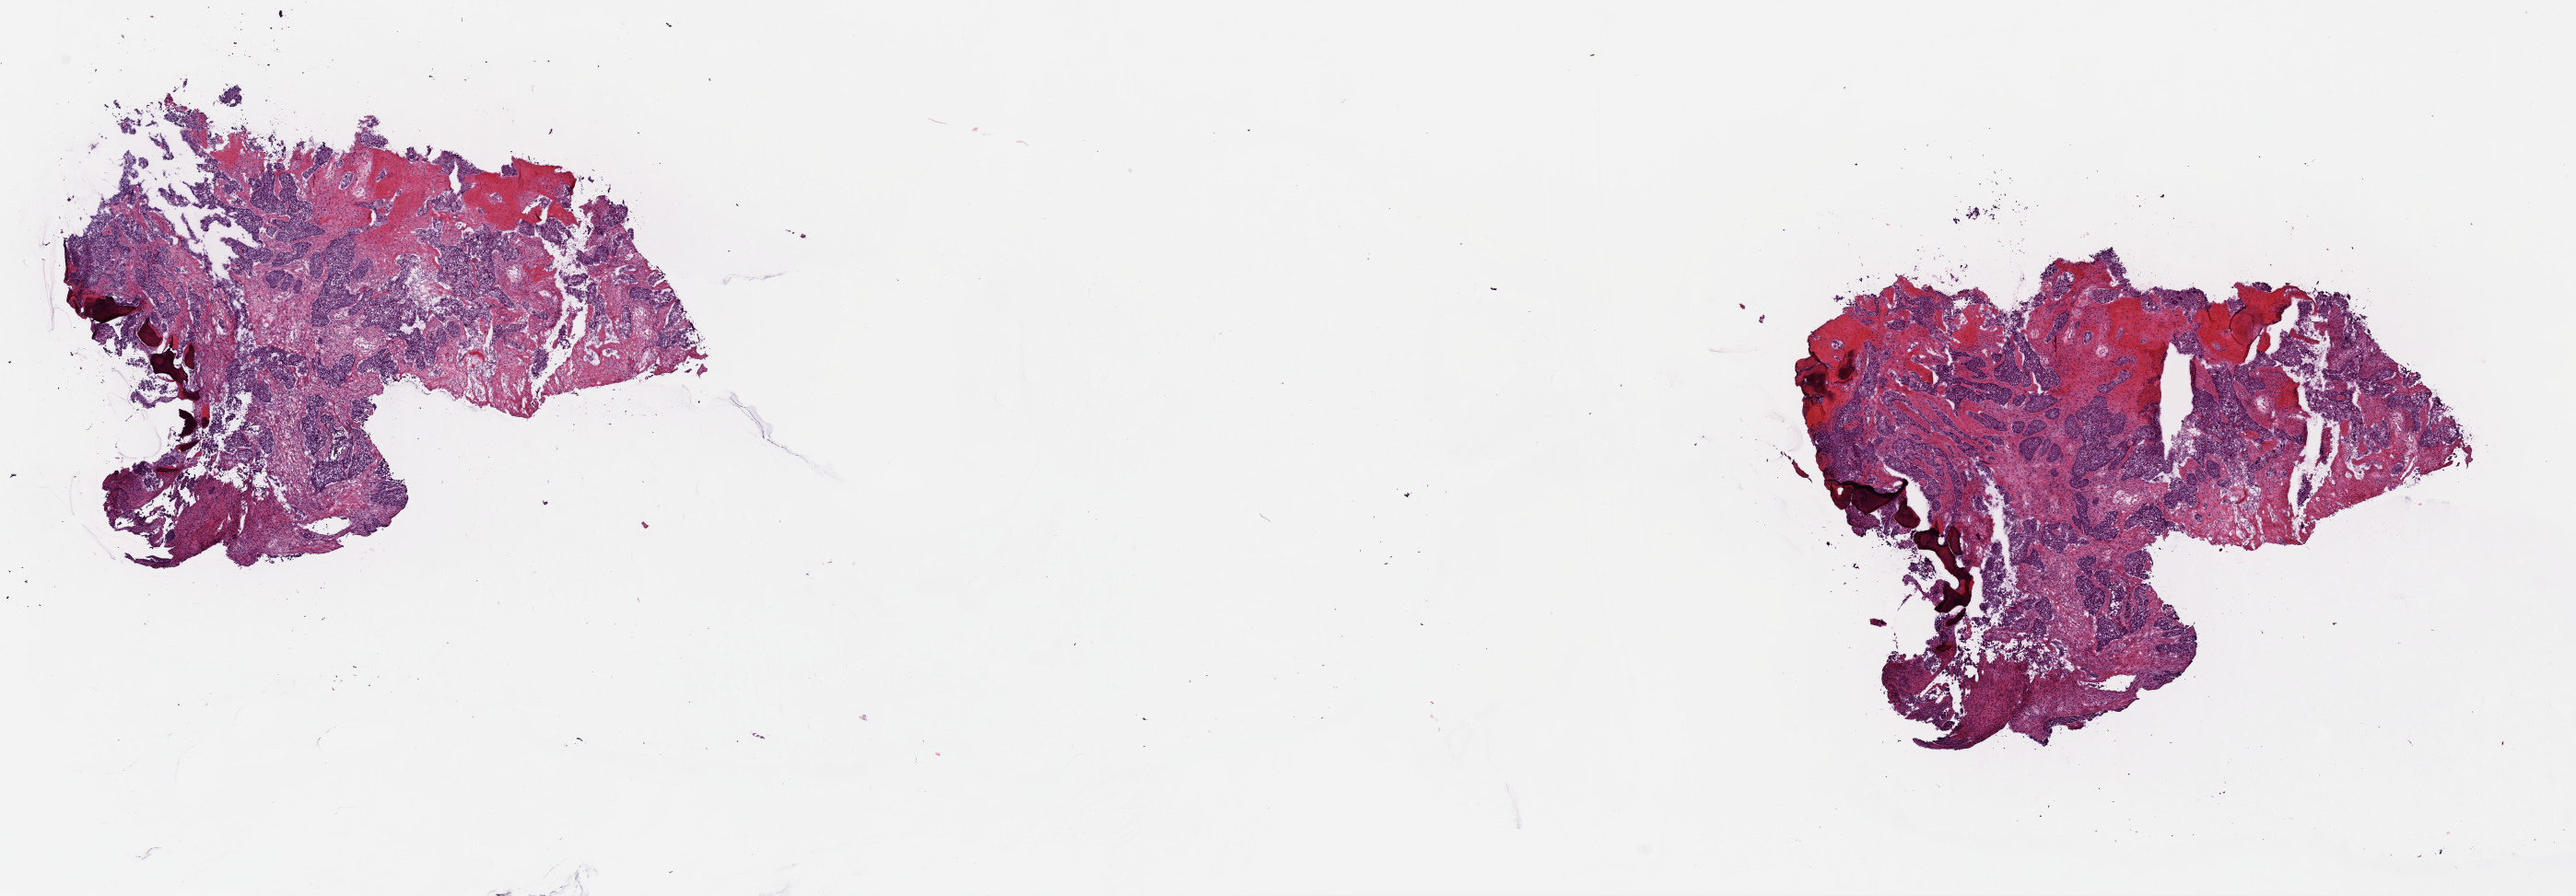
Hematoxylin and eosin (H&E) stained whole-slide image — shown as a low-resolution overview of the whole scanned area (about 22.1 x 7.7 mm, from a 40x scan); frozen section; primary tumour sample from the breast. Patient: female, age at initial diagnosis 58 years. Composition of this section per pathologist review: tumour cells 55%, tumour nuclei 80%, normal cells 0%, stromal cells 42%, necrosis 3%. Inflammatory infiltration, as recorded: lymphocyte infiltration 1%, monocyte infiltration 0%, neutrophil infiltration 0%.
AJCC pathologic stage: IIB. Pathologic diagnosis: Infiltrating duct carcinoma, NOS.